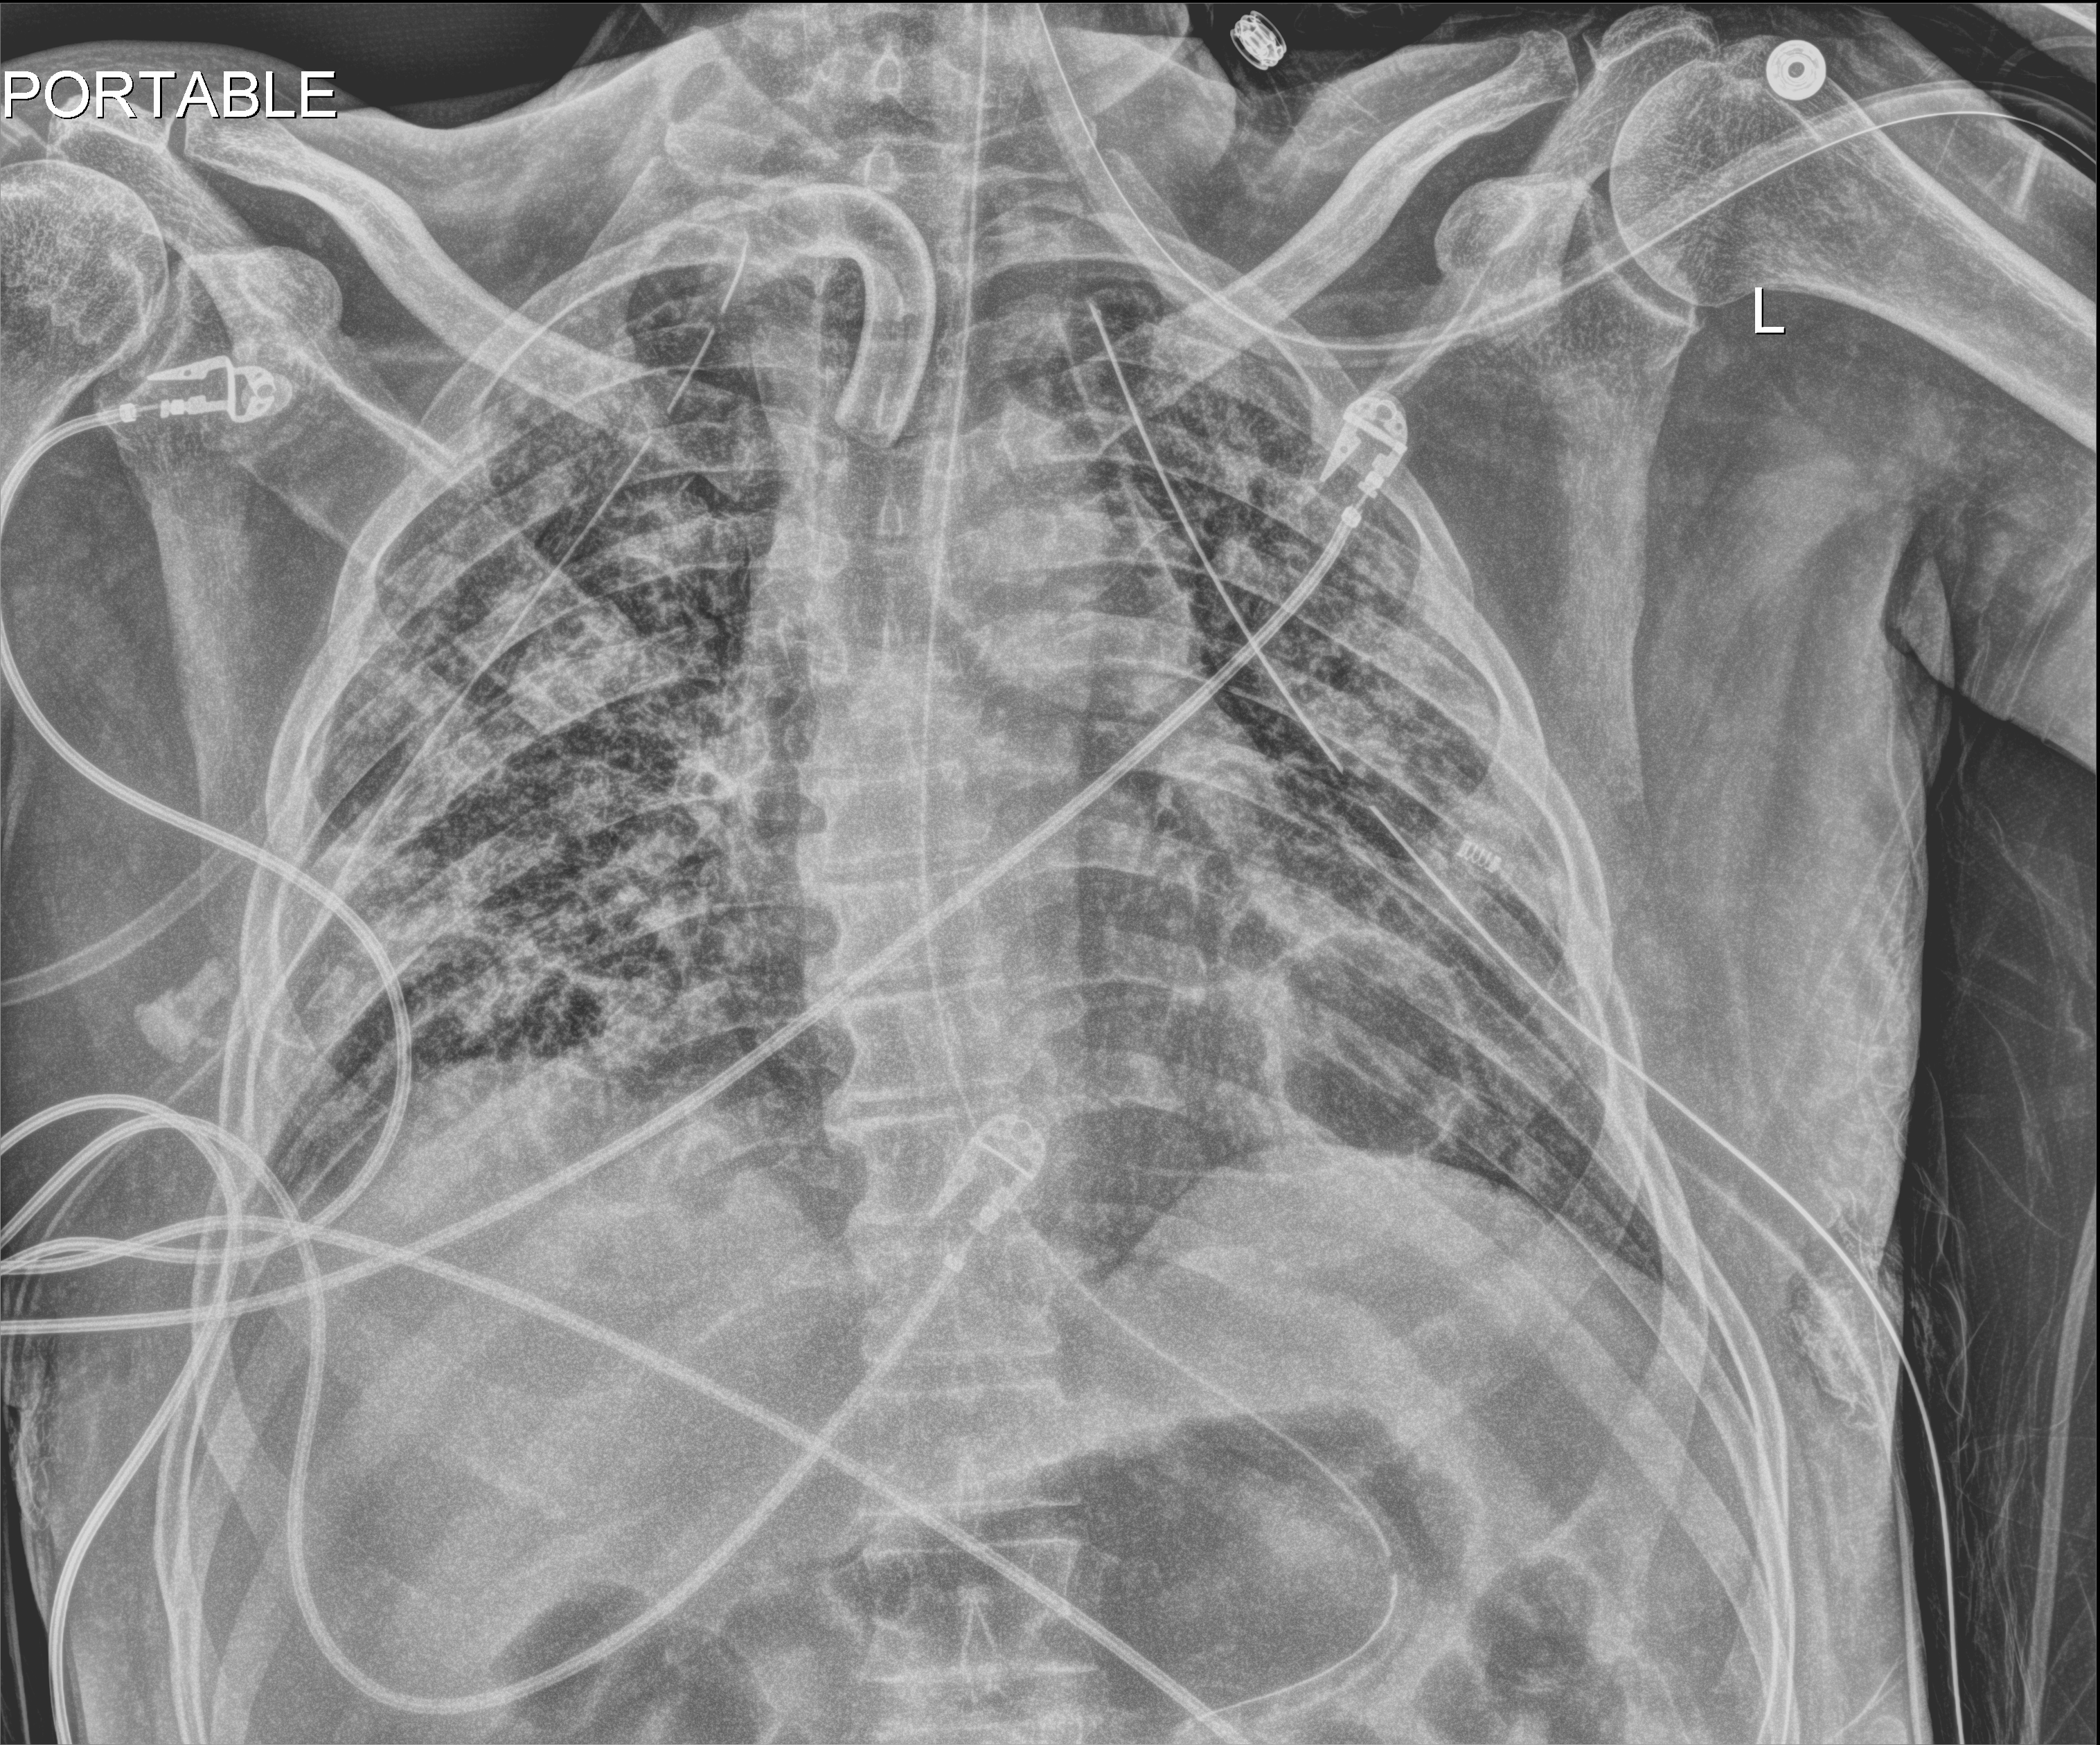
Portable chest radiograph, anteroposterior (AP) projection. Male patient hospitalised with COVID-19, age 18–59 years.
Admission-level facts for this patient (not findings on this image; timing relative to this image not recorded):
- mechanically ventilated during this hospital stay: yes
- admitted to intensive care during this hospital stay: yes